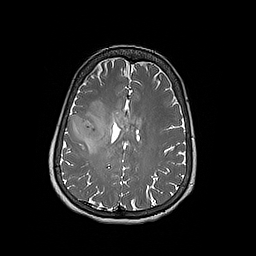
Brain MRI from a brain-tumour surgery series, one axial slice; slice 76 of 192 in the series (ordered by position); 1 mm slice thickness; 256 × 256 image matrix. Case-level facts recorded for this patient, not image findings: histopathology: Oligodendroglioma; WHO grade: 3; IDH mutation: yes.
Structures marked on this image (expert manual segmentation):
- tumour: bounding box (x1, y1, x2, y2) in pixels: (68, 114, 107, 148)